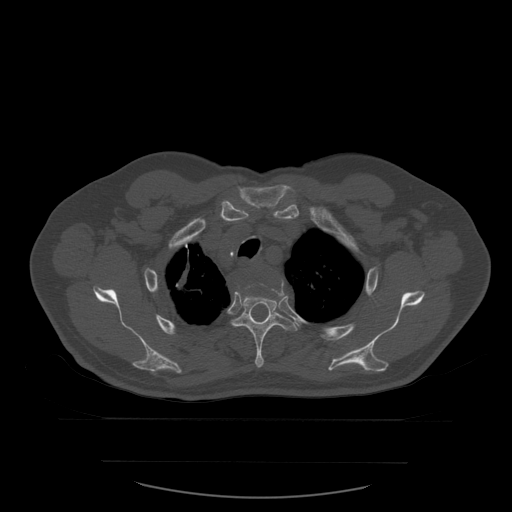
CT including the spine, one axial slice. Slice 446 of 590 in the series (ordered by position). Bone window (W 1800 / L 400 HU). 512 × 512 image matrix, field of view 479 × 479 mm. Patient age 71 years. Case-level facts recorded for this patient, not image findings: primary cancer: lung.
Annotated regions visible in this slice (semi-automatically segmented with operator editing):
- T3 vertebra: box from (x=243, y=279) to (x=284, y=295) px
- T4 vertebra: (x=231, y=283)–(x=298, y=368)